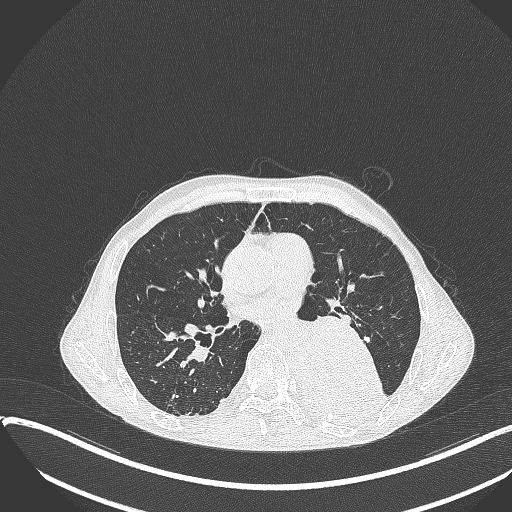
Chest CT, one axial slice; slice 190 of 401 in the series (ordered by position); lung window (W 1500 / L -600 HU); 1 mm slice thickness; 512 × 512 image matrix, field of view 400 × 400 mm. Patient: male, 57 years. From the clinical record (not read from this slice): clinical TNM (as recorded): T4 N0 M0.
Annotated regions visible in this slice (bounding box drawn by a radiologist):
- lung tumour (recorded histology: squamous cell carcinoma): bounding box <289,314,386,421> (left, top, right, bottom; pixels)